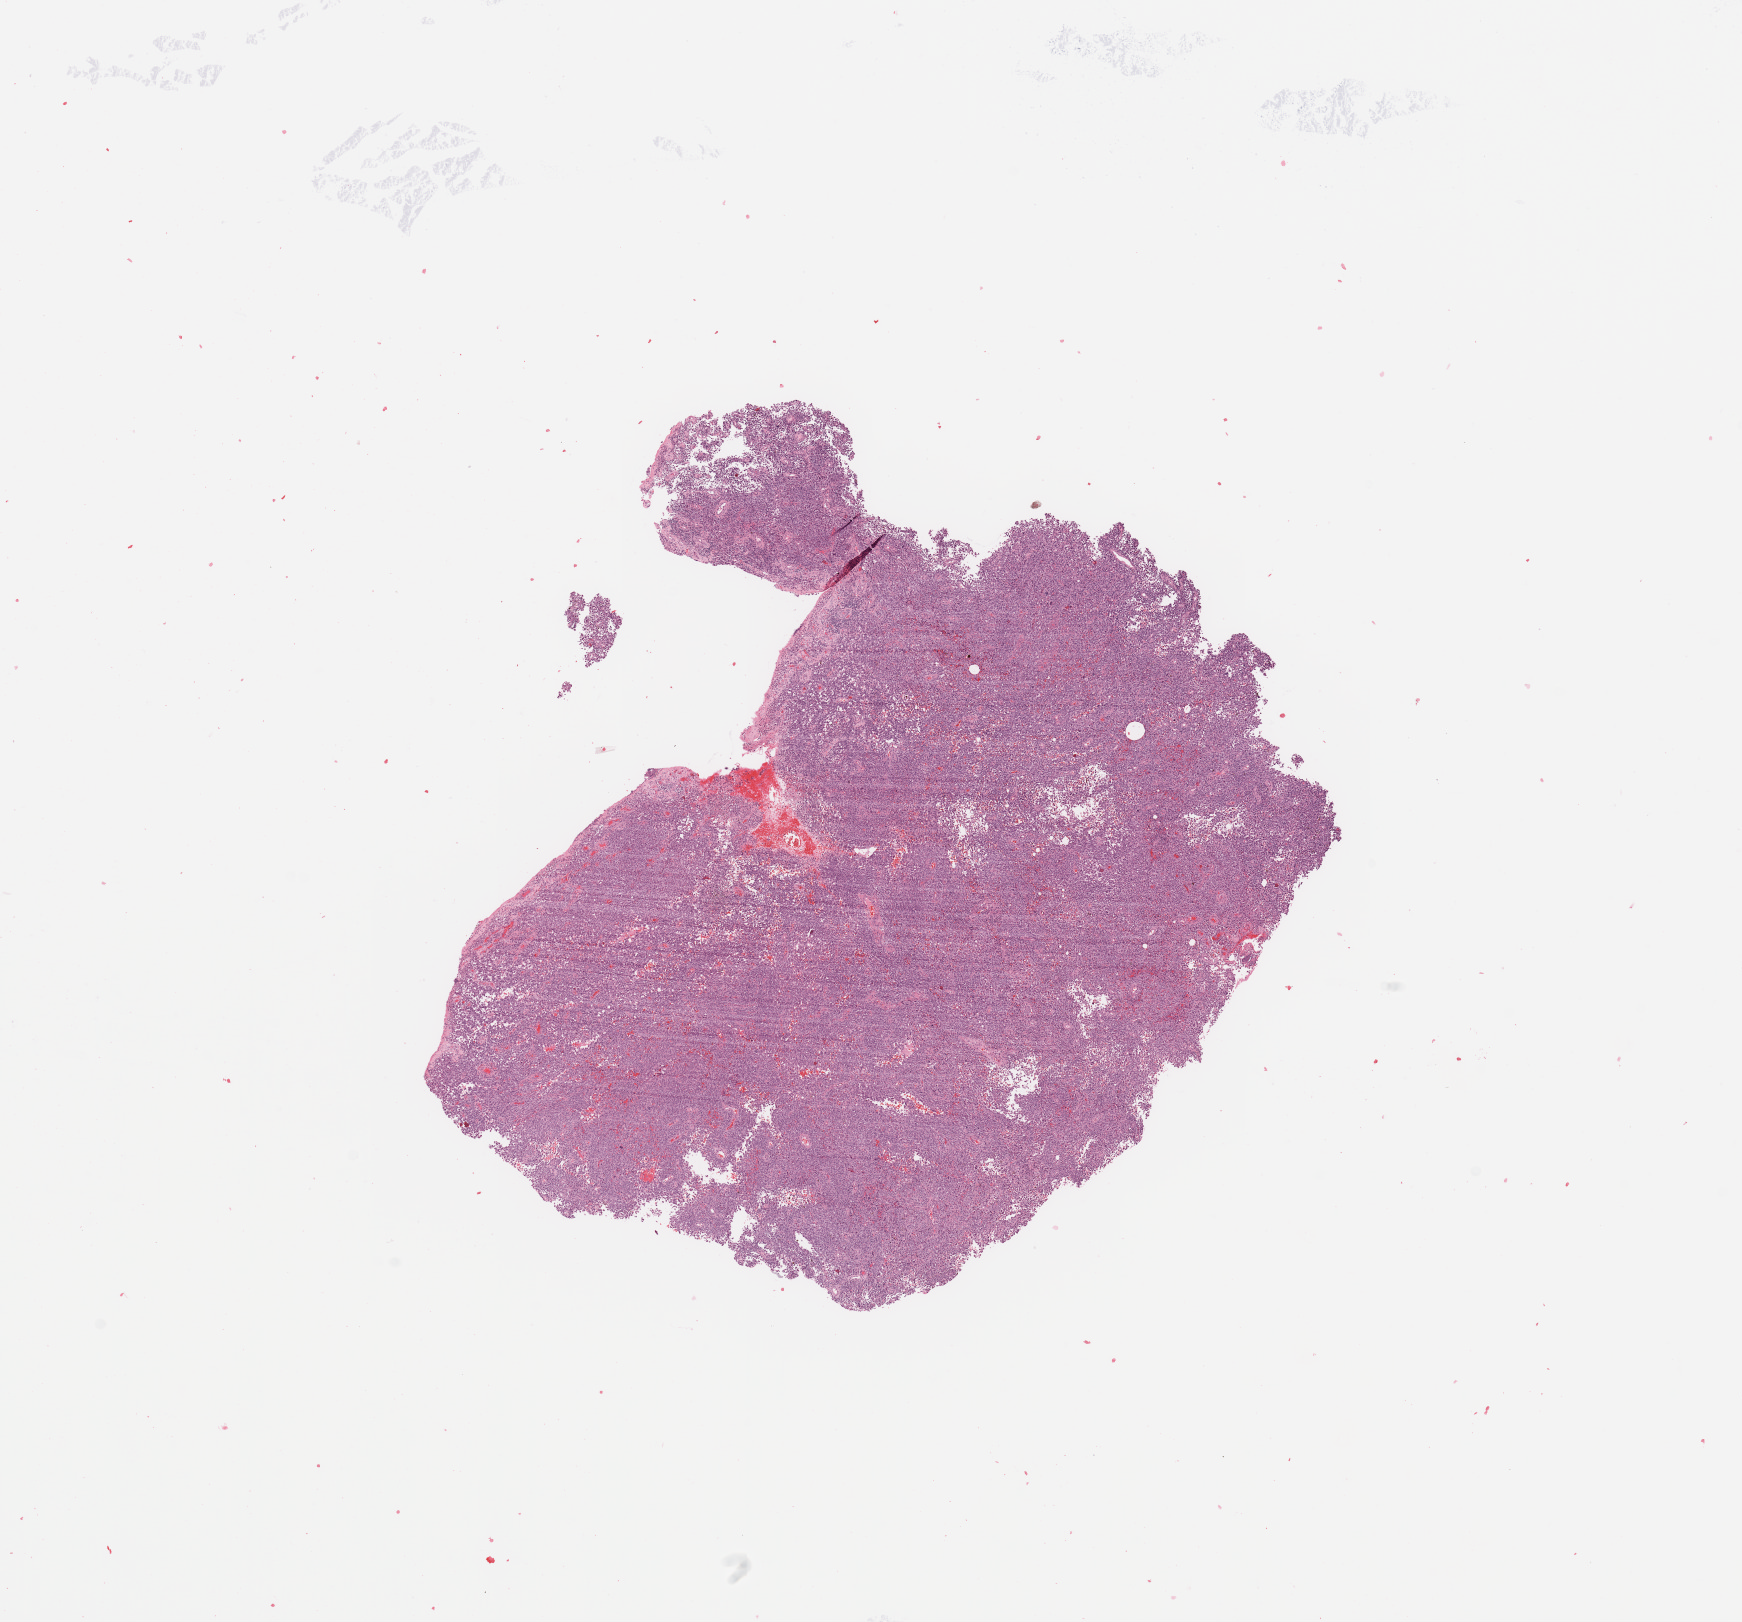
Digitized H&E-stained tissue section (whole slide), whole scanned area (about 13.8 x 12.8 mm, acquisition: 20x scan) shown as a low-resolution overview; melanoma tumour tissue; sampled site not recorded. Patient: male, age 34 years.
AJCC pathologic stage: IIIB. Primary tumour site (as recorded): trunk. Histologic diagnosis: Malignant melanoma, NOS.